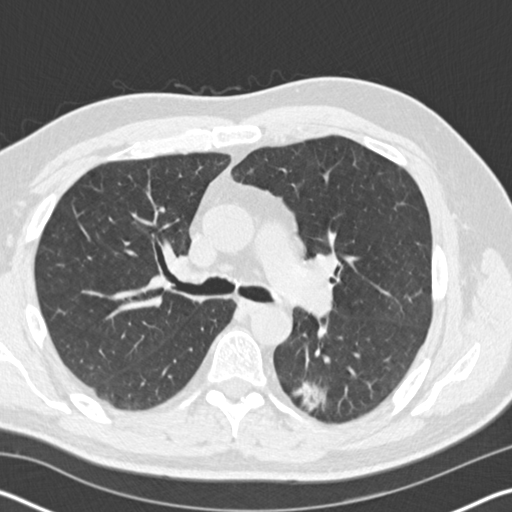
Low-dose screening chest CT, one axial slice; position 108 of 178 along the scan axis; lung window (W 1500 / L -600 HU); 2 mm slice thickness; 512 × 512 image matrix, field of view 340 × 340 mm.
Annotated regions visible in this slice (expert manual segmentation):
- lesion 1 (tumor, lower lobe of left lung): bounding box [x1, y1, x2, y2] px = [293, 383, 326, 411]